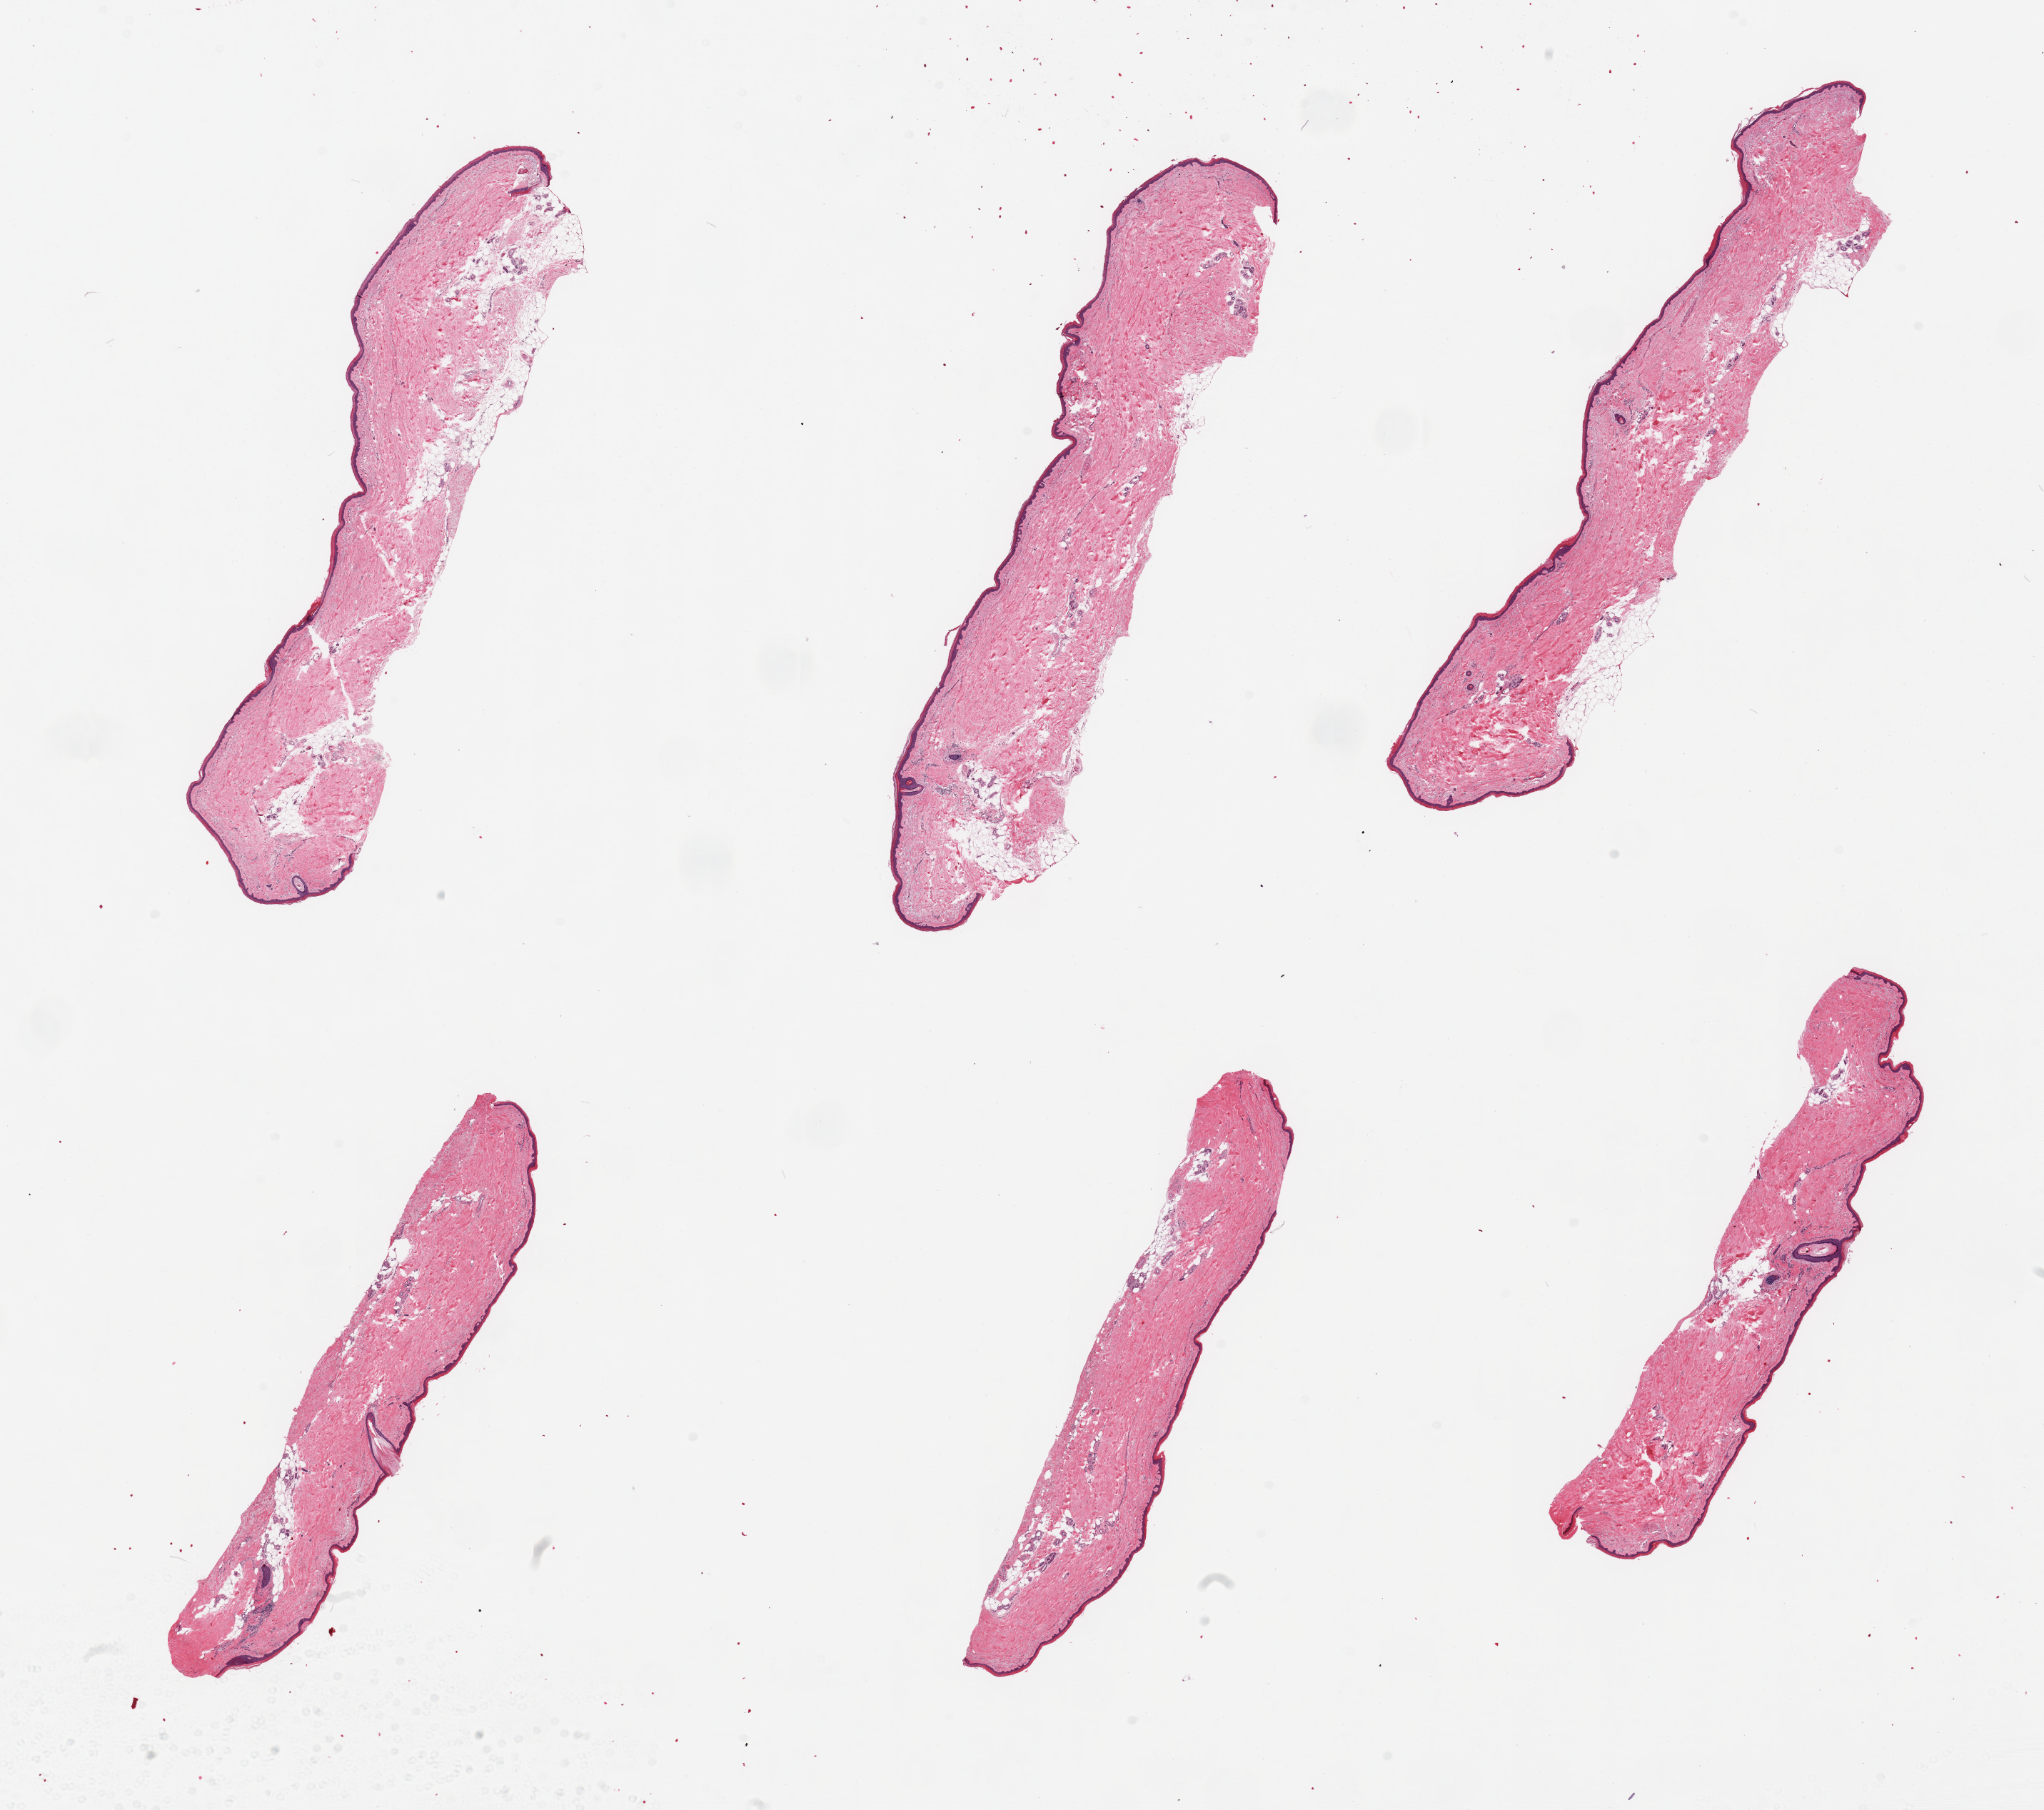
Digitized haematoxylin and eosin-stained section, whole scanned area (about 22.6 x 20.0 mm) shown as a low-resolution overview; PAXgene-fixed, paraffin-embedded tissue; sampled site (target tissue): skin of lower leg; donor tissue sample. Donor sex: female.
Reviewer comment on this tissue sample: 6 pieces, no dermal fat; squamous epithelium is ~25 microns.